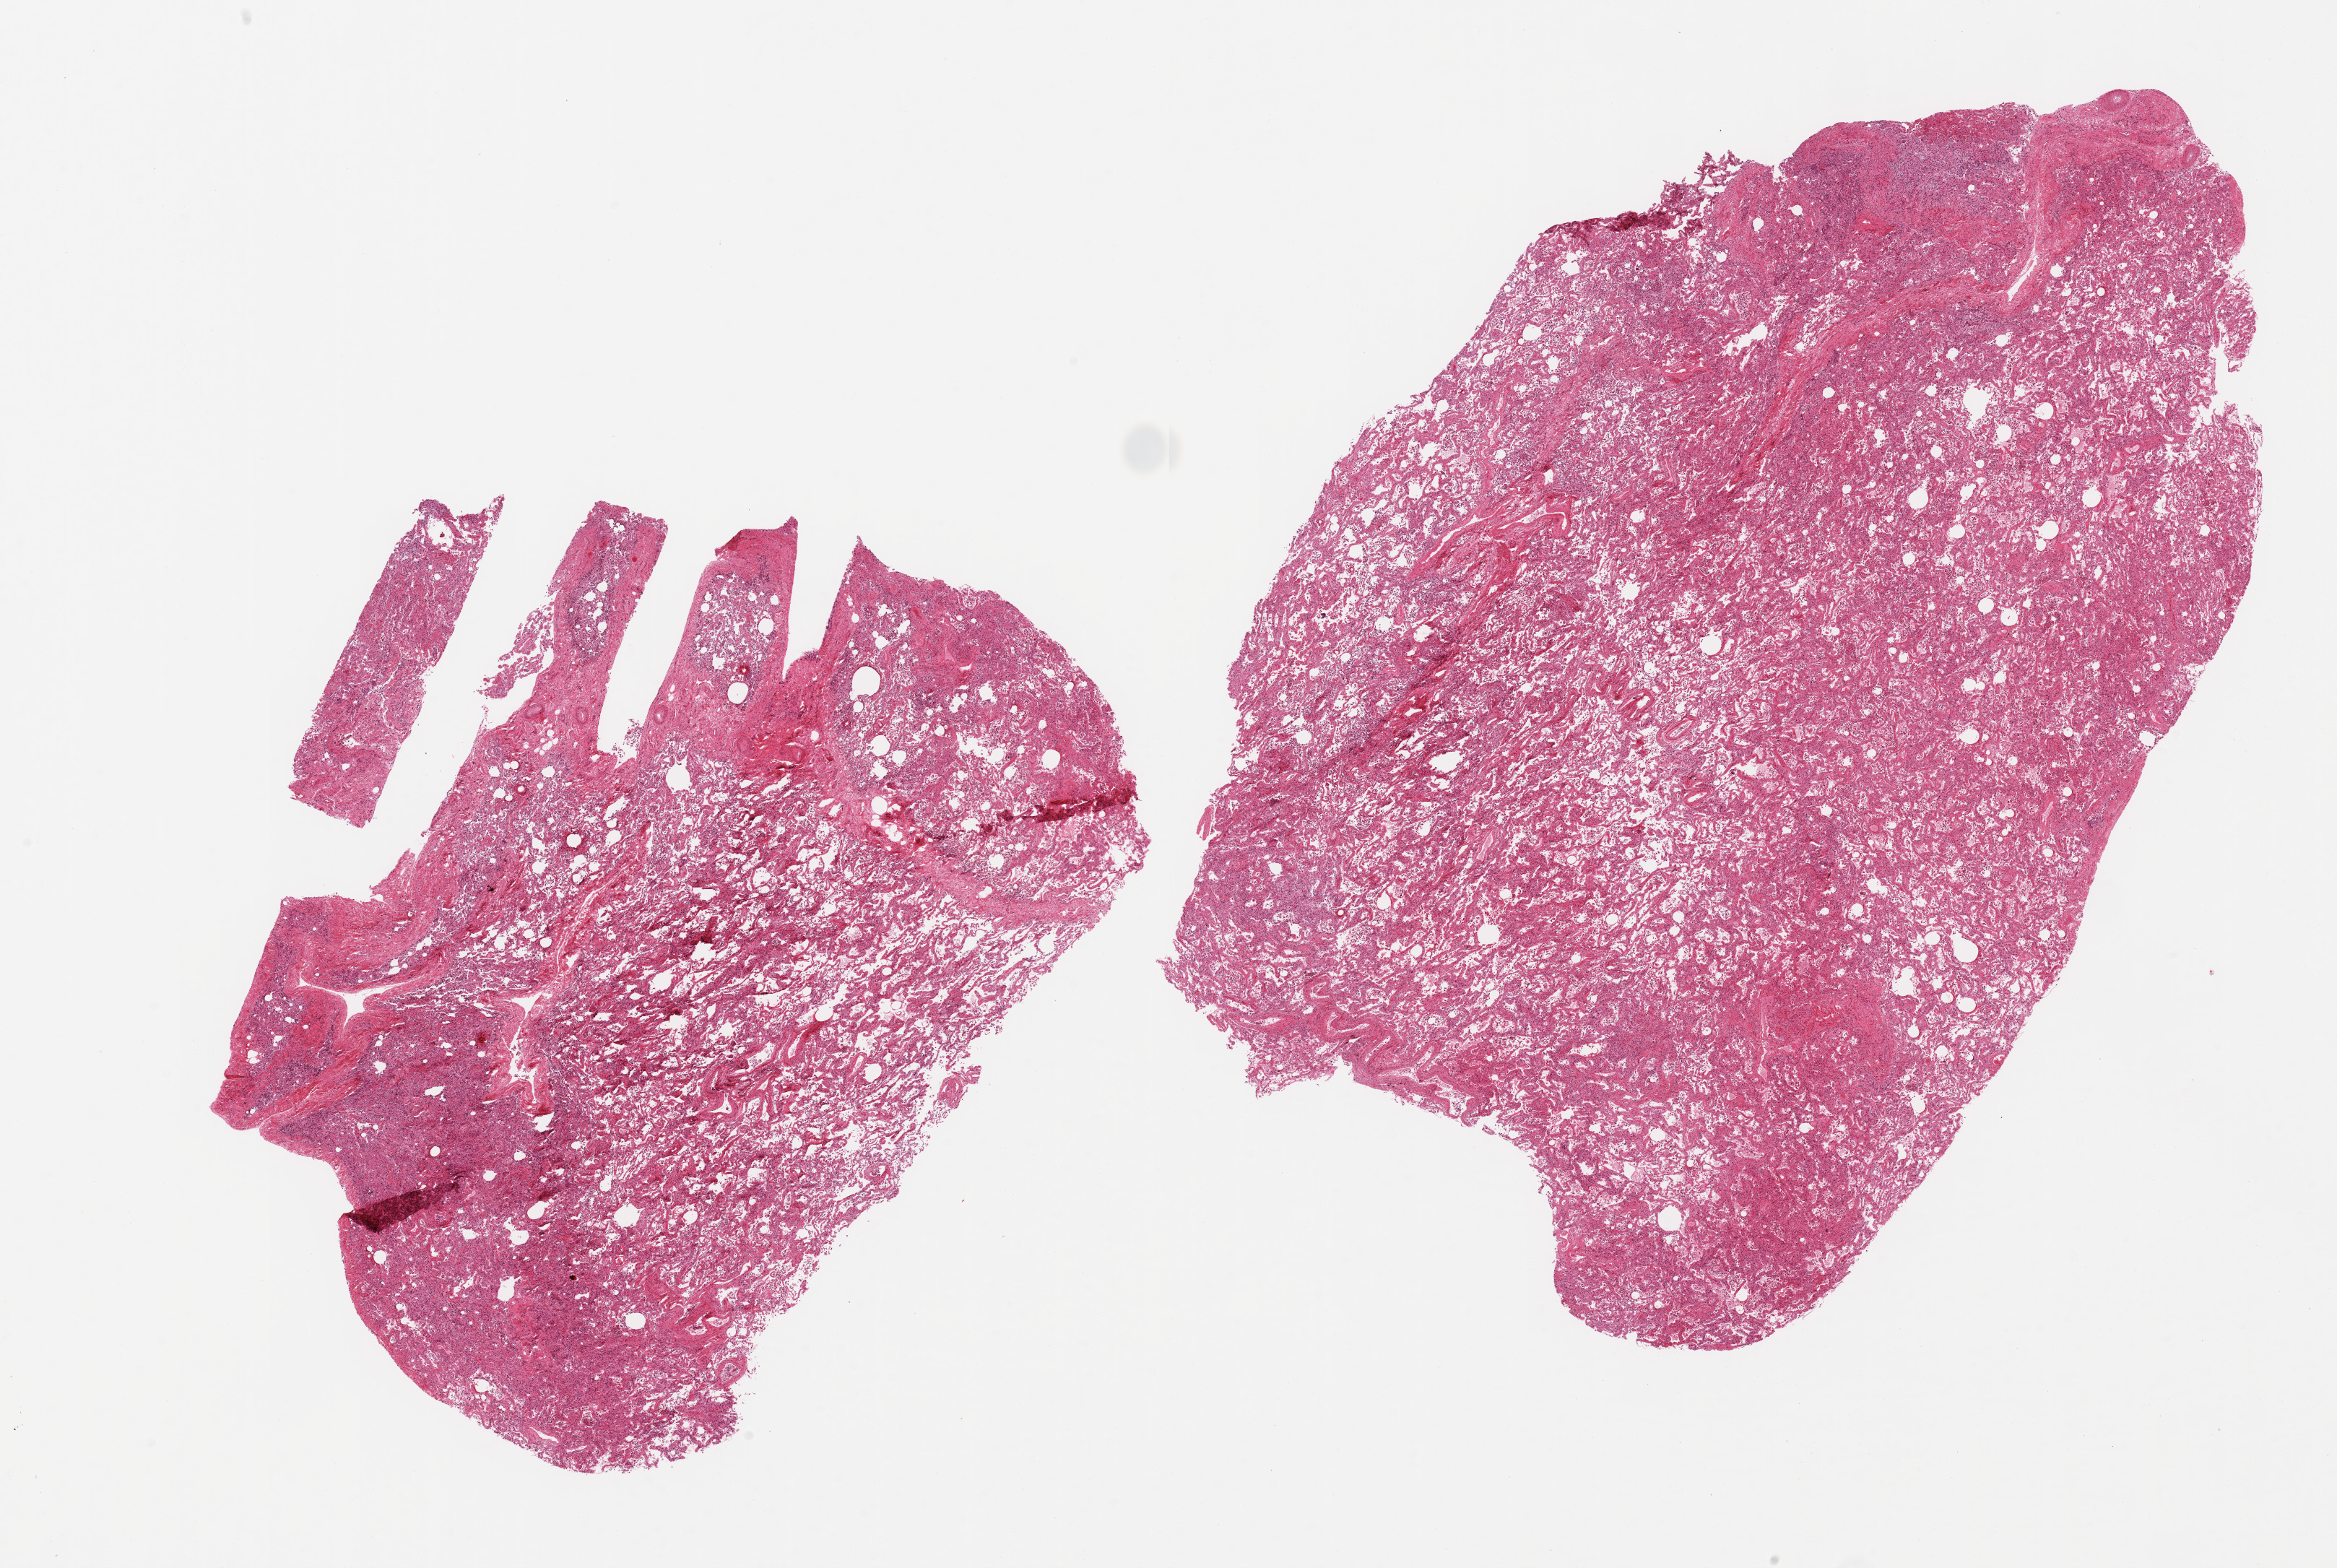
Digitized haematoxylin and eosin-stained section — low-resolution overview of the scanned area, about 25.6 x 17.2 mm (slide scanned at 20x), PAXgene-fixed, paraffin-embedded tissue, target tissue: lung, donor tissue sample. Donor sex: male.
• reviewer comment on this tissue sample: 2 pieces; severe arterial hypertrophy with interstitial fibrosis consistent with clinical history of pulmonary scleroderma